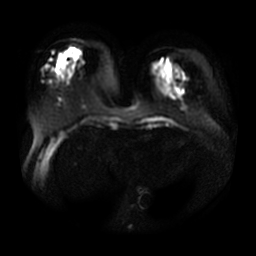
Breast MRI, one axial slice. Position 10 of 29 along the scan axis. Diffusion-weighted series; image 2 of 4 stored at this slice position (different b-values; order by instance number). 3 T. 256 × 256 image matrix, field of view 380 × 380 mm. Female patient.
Structures marked on this image (expert manual segmentation):
- tumour on diffusion-weighted imaging: box from (x=68, y=50) to (x=71, y=54) px